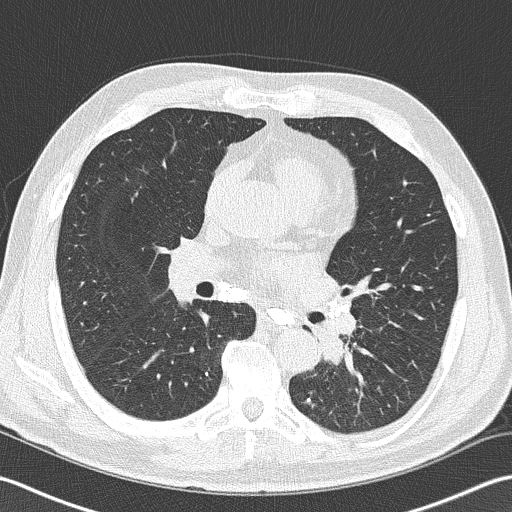
Low-dose screening chest CT, axial slice; second annual screen; lung window (W 1500 / L -600 HU); slice 77 of 170 in the series. Male participant, aged 57 years at enrolment. Former smoker at enrolment.
Expert-annotated lung lesion, bounding box [x1, y1, x2, y2] px = [293, 299, 373, 380]. Reader record for this screening exam (exam-level; its link to the box is not recorded): non-calcified nodule or mass ≥4 mm, left lower lobe, 40 × 30 mm, spiculated (stellate) margins, soft tissue attenuation, pre-existing on the prior screen: no. Official screen result: positive, other. Participant outcome: lung cancer diagnosed 9 days after this screen — squamous cell carcinoma, NOS, left lower lobe, moderately differentiated (G2), stage IIIB (AJCC 6th edition), 38 mm at pathology.